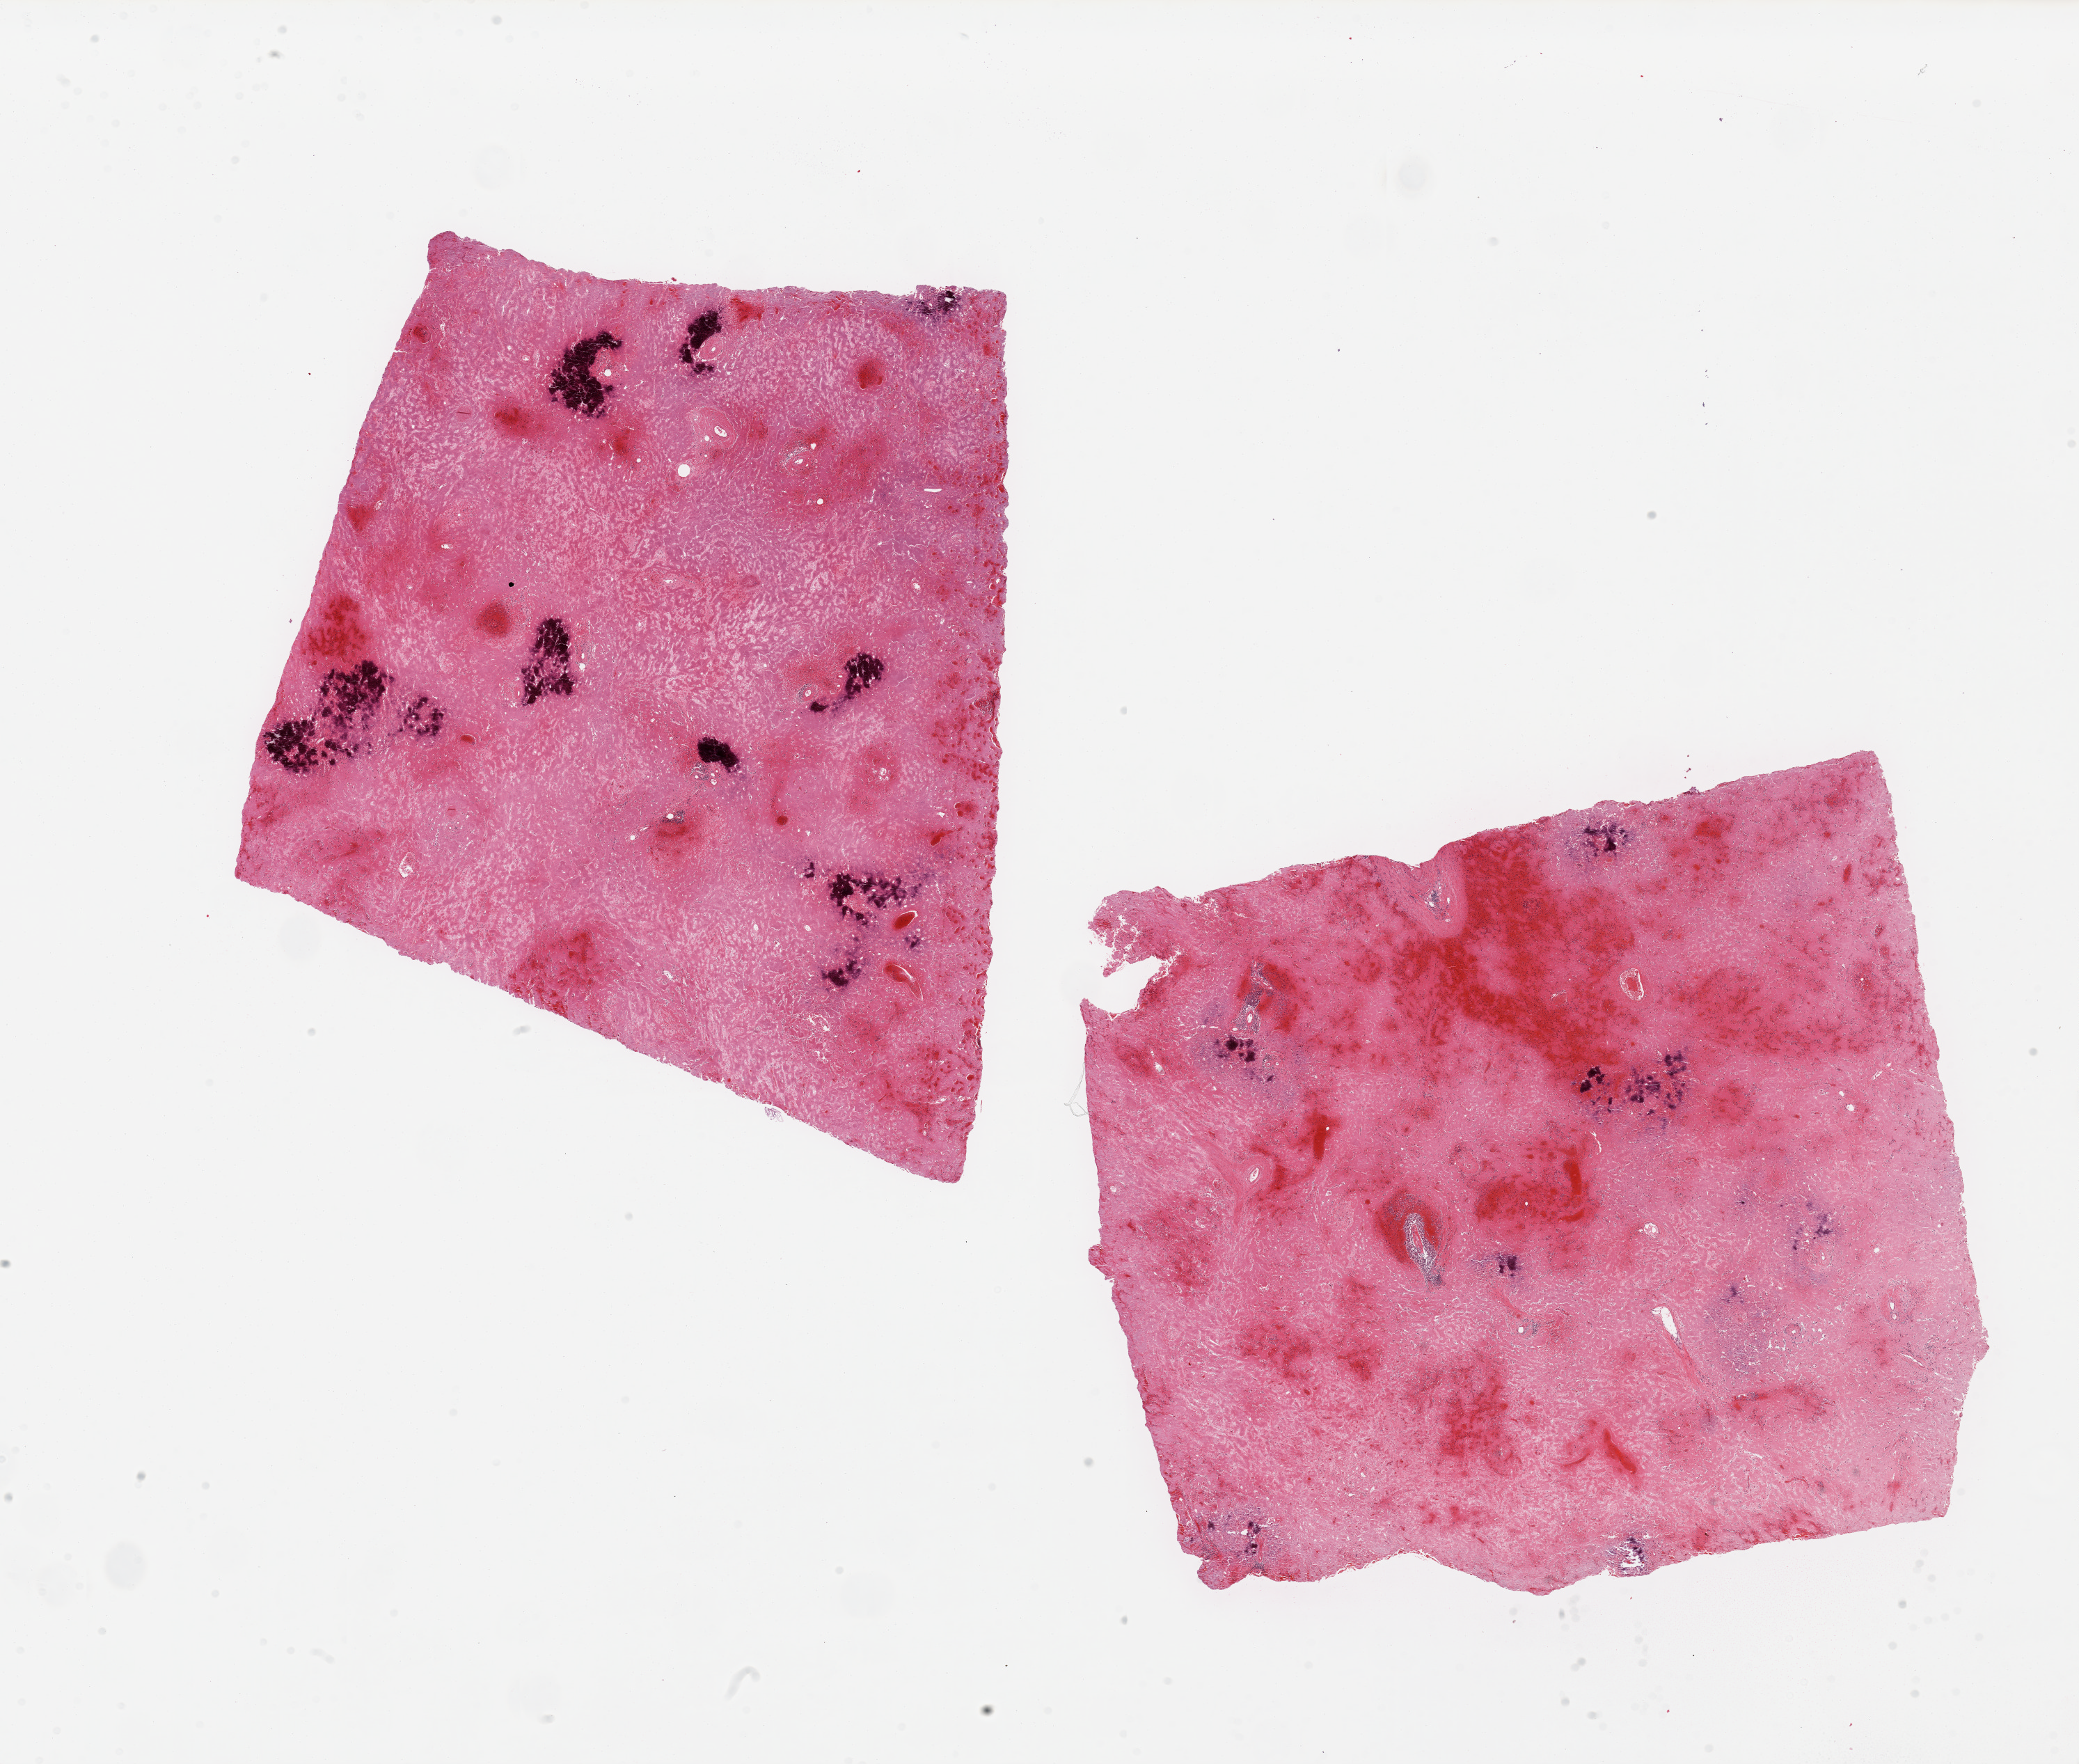
Hematoxylin and eosin (H&E) whole-slide image, brightfield, a low-resolution overview of the entire scanned area, about 23.6 x 20.0 mm, PAXgene-fixed paraffin-embedded (PFPE) section, target tissue: spleen, donor tissue sample. Male donor.
Review note (as recorded): 2 pieces, diffuse waxy infiltrate, suggestive of amyloid.